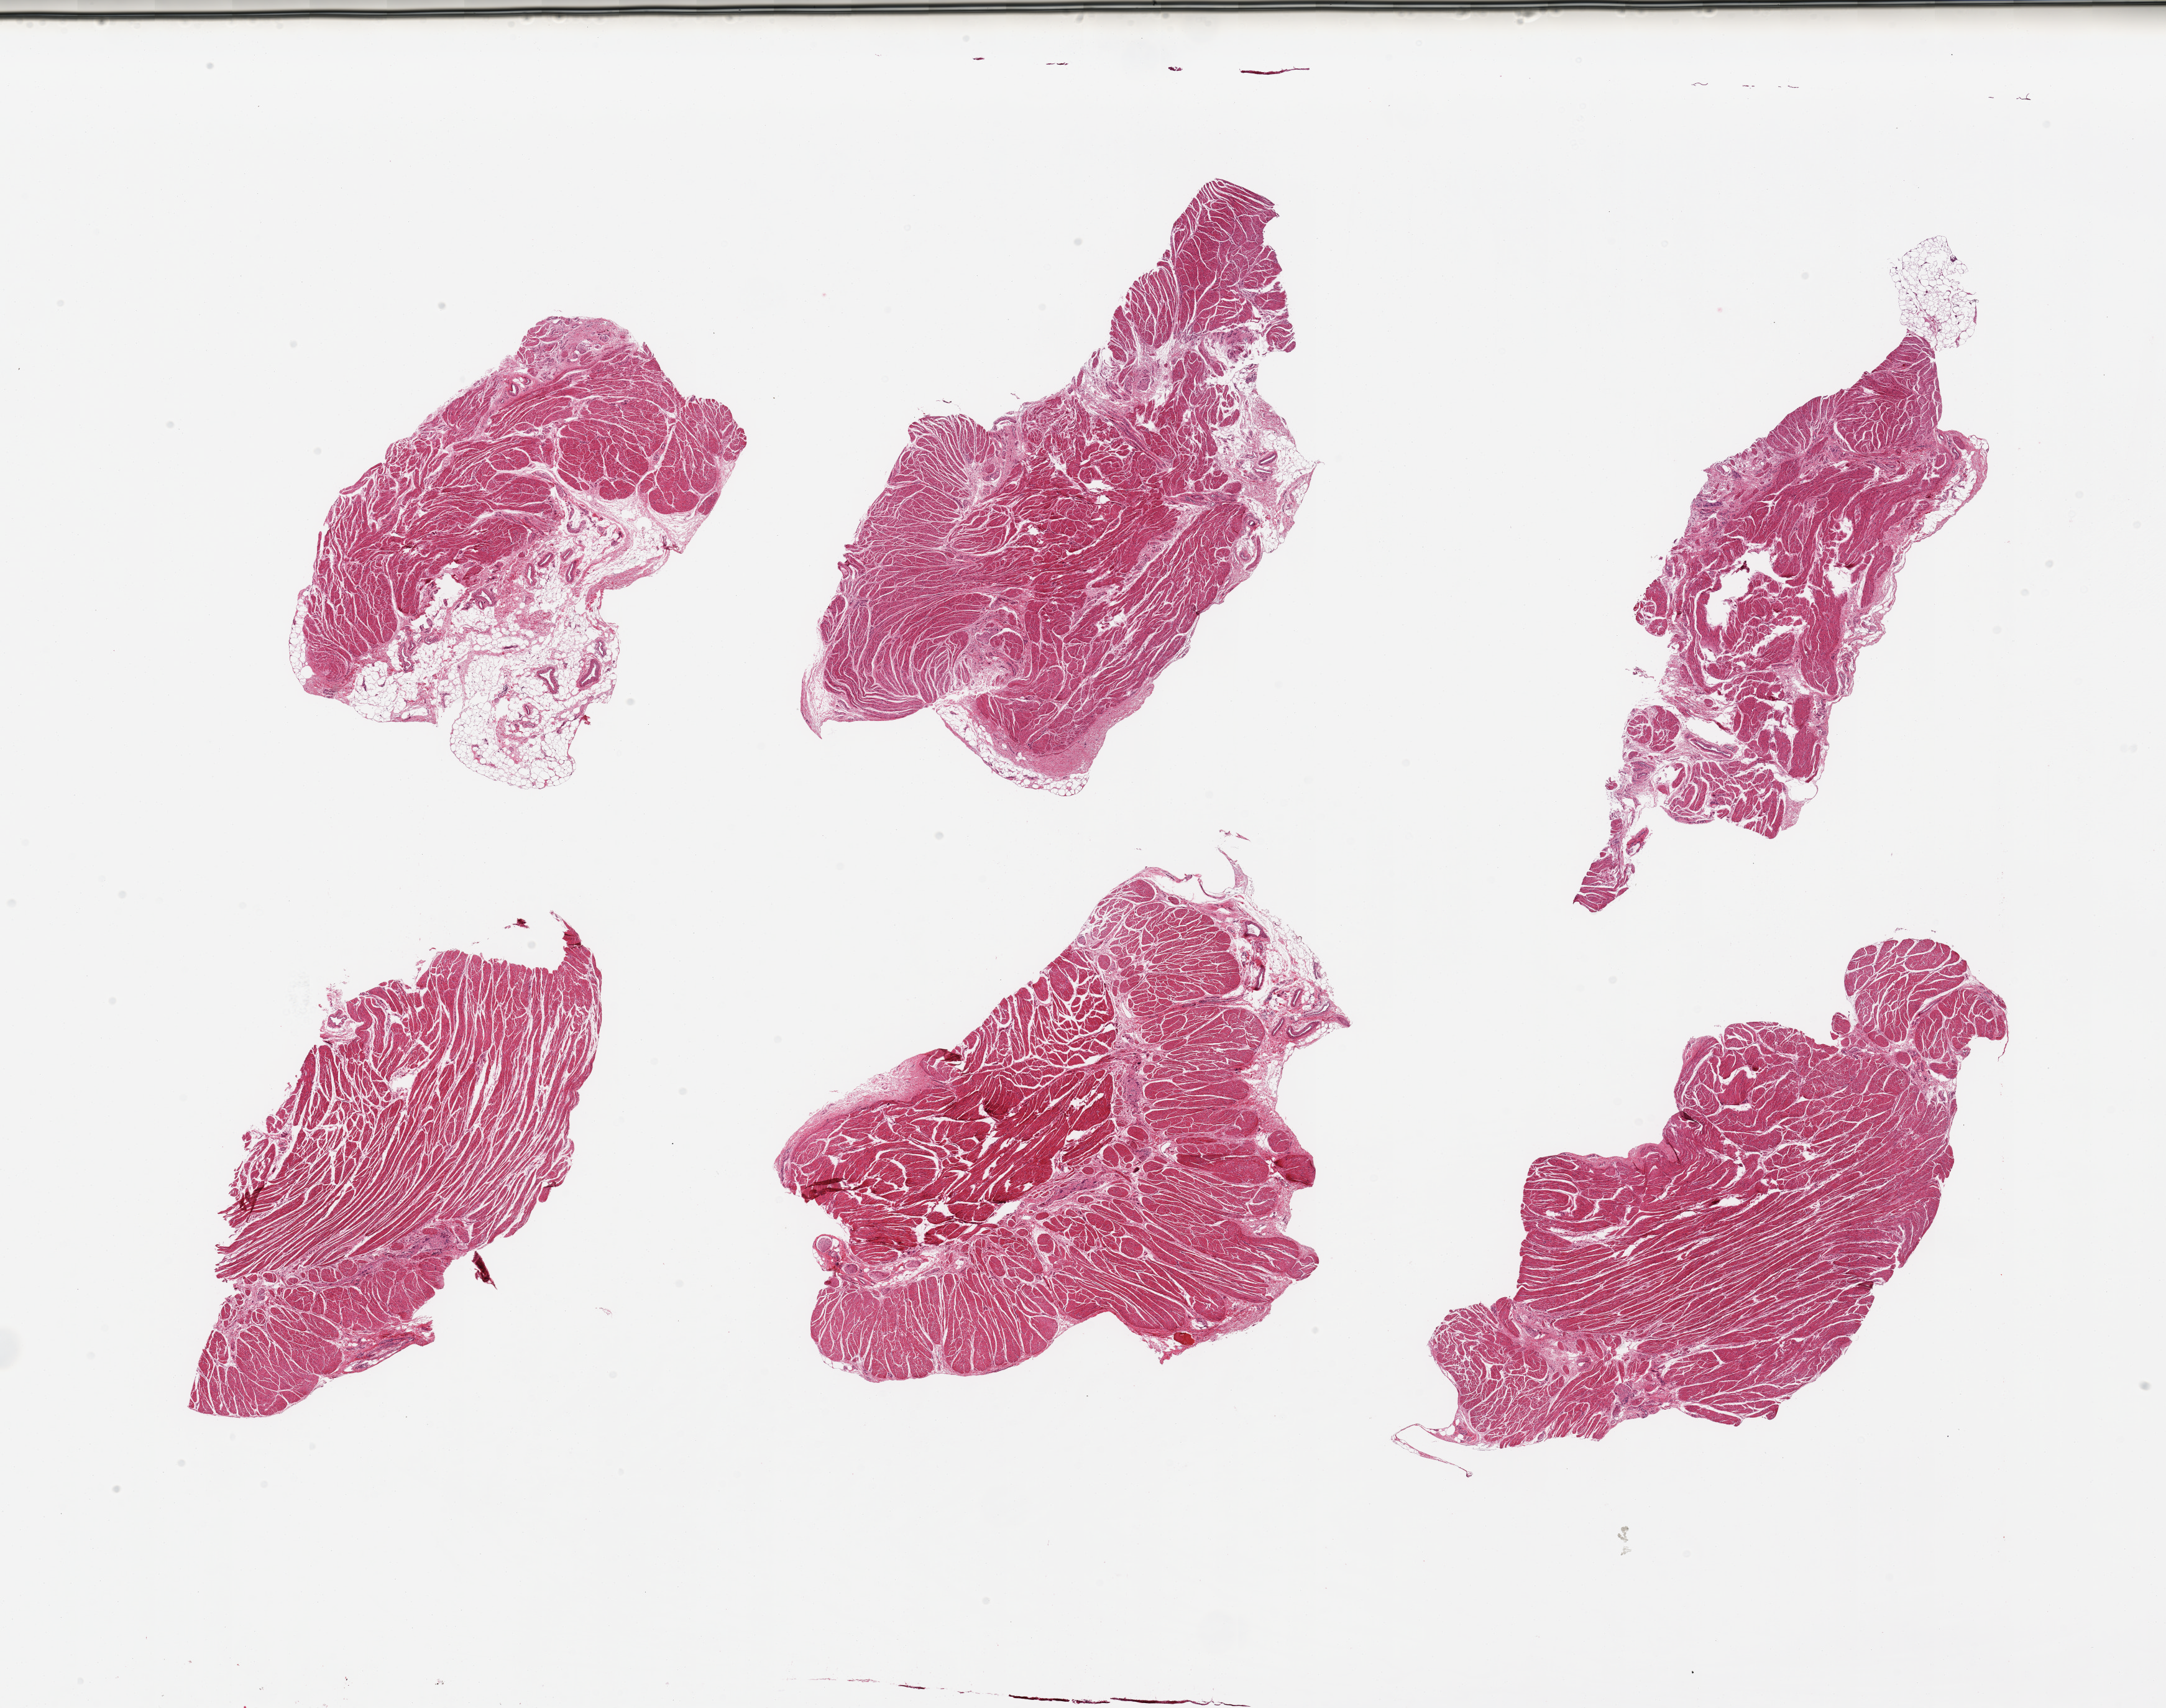
Digitized H&E-stained section, shown as a low-resolution overview of the whole scanned area (about 27.6 x 21.7 mm). PAXgene-fixed paraffin-embedded (PFPE) section. Sampled site (target tissue): gastroesophageal junction. Donor tissue sample. Donor sex: female.
Reviewer comment on this tissue sample: 6 pieces; well trimmed except for 1 piece with 30% submucosa.